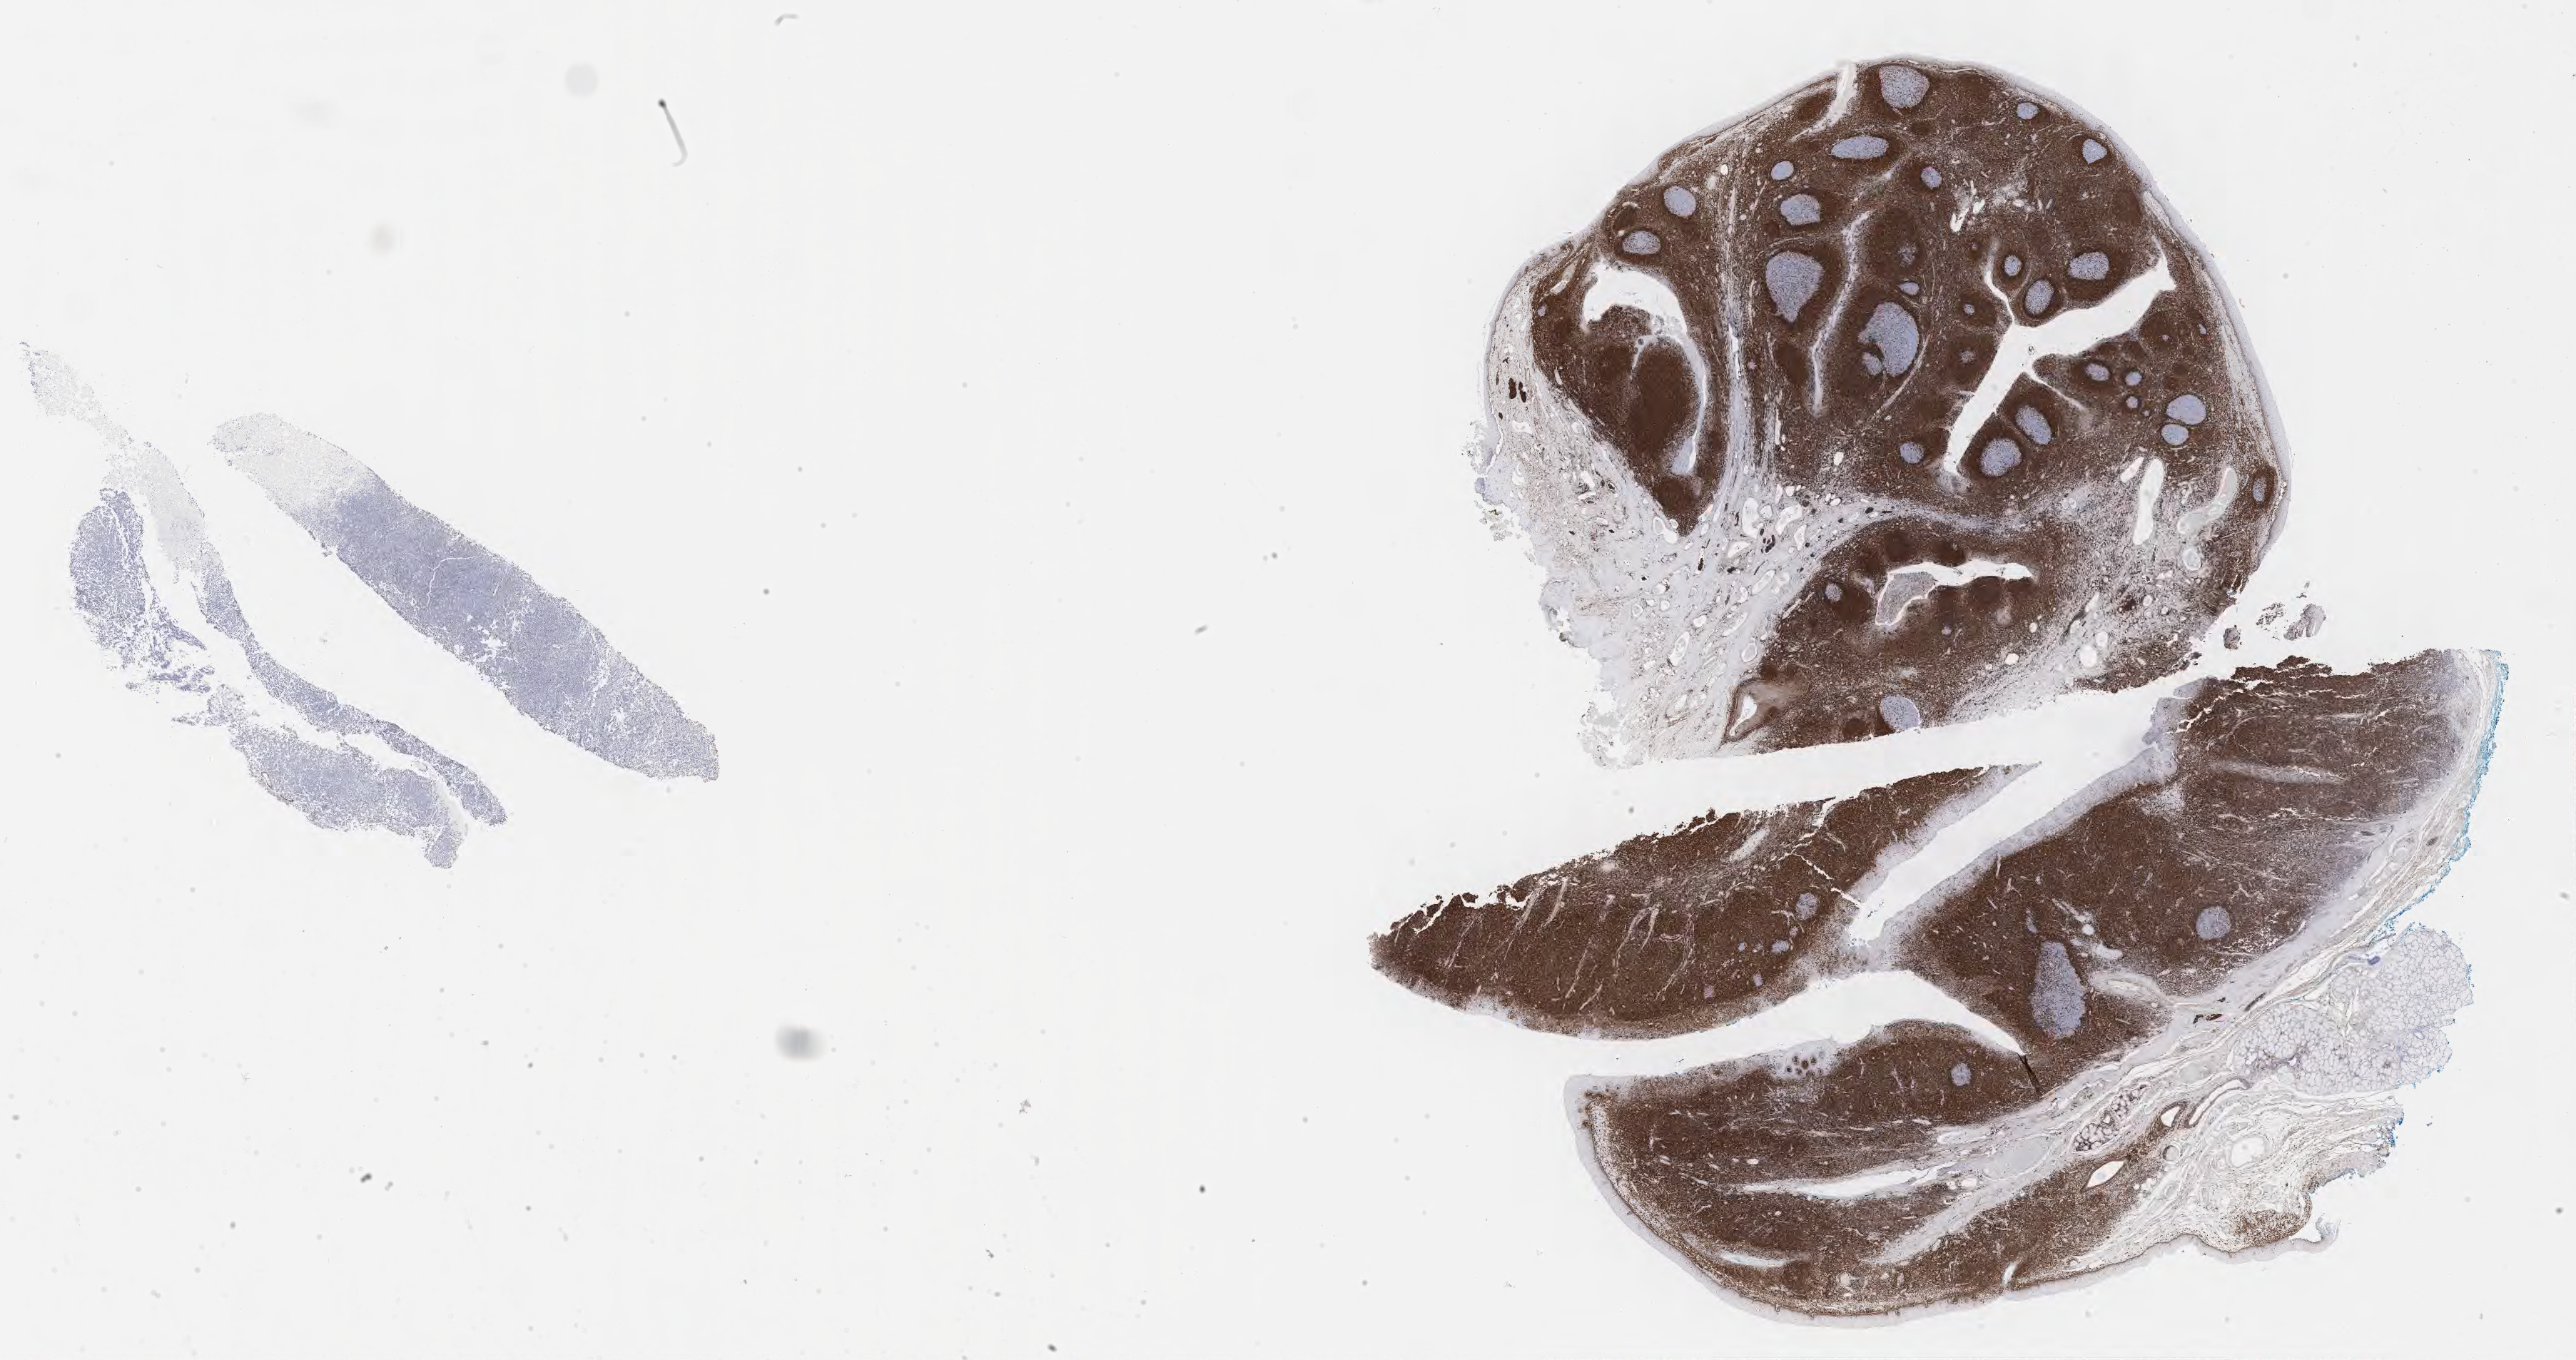
IHC for BCL2, whole-slide image, shown as a low-resolution overview of the whole scanned area (about 29.2 x 15.4 mm). Tumor tissue. Patient: female, age 18 years.
- histologic diagnosis: Burkitt lymphoma, NOS